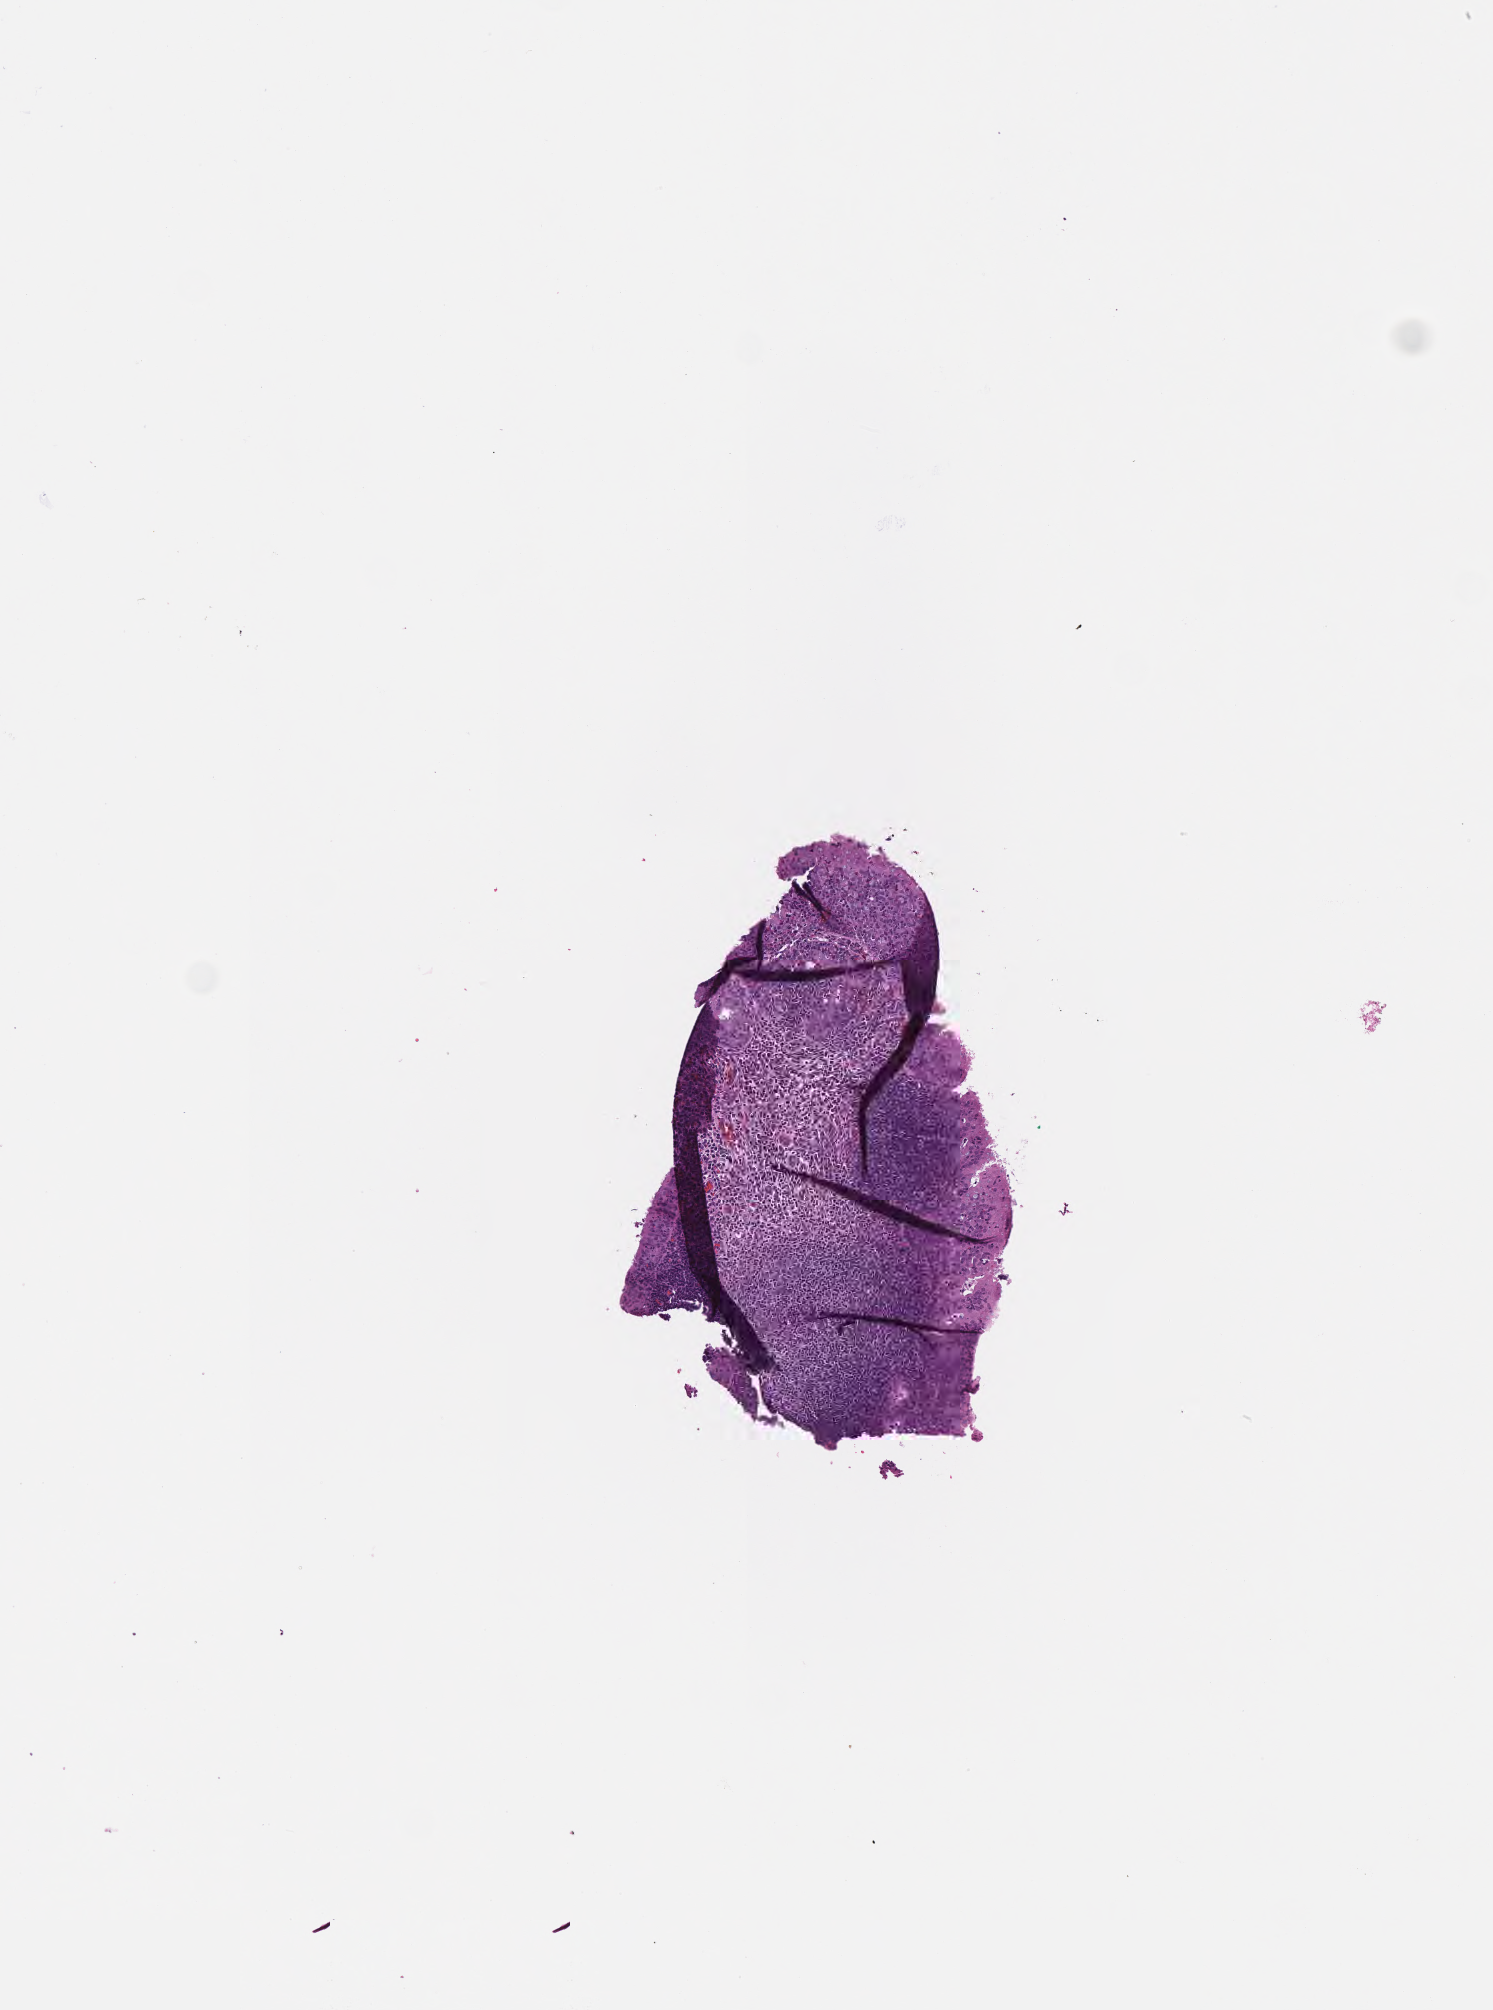
Whole-slide image, haematoxylin and eosin stain, shown as a low-resolution overview of the whole scanned area (about 3.0 x 4.1 mm); FFPE section; specimen: non-tumor (normal tissue) sample from a patient with burkitt lymphoma, NOS. Patient: male, age at initial diagnosis 5 years. Pathologist review of this section (percent, as recorded): tumor cells 0%, tumor nuclei 0%, stromal cells 0%, necrosis 0%, normal cells 100%. Infiltration values recorded for this section: lymphocyte infiltration 75%, monocyte infiltration 15%, neutrophil infiltration 5%.
This section: non-tumor tissue sample; the patient's diagnosis is given above. Section: bottom of the tissue portion.